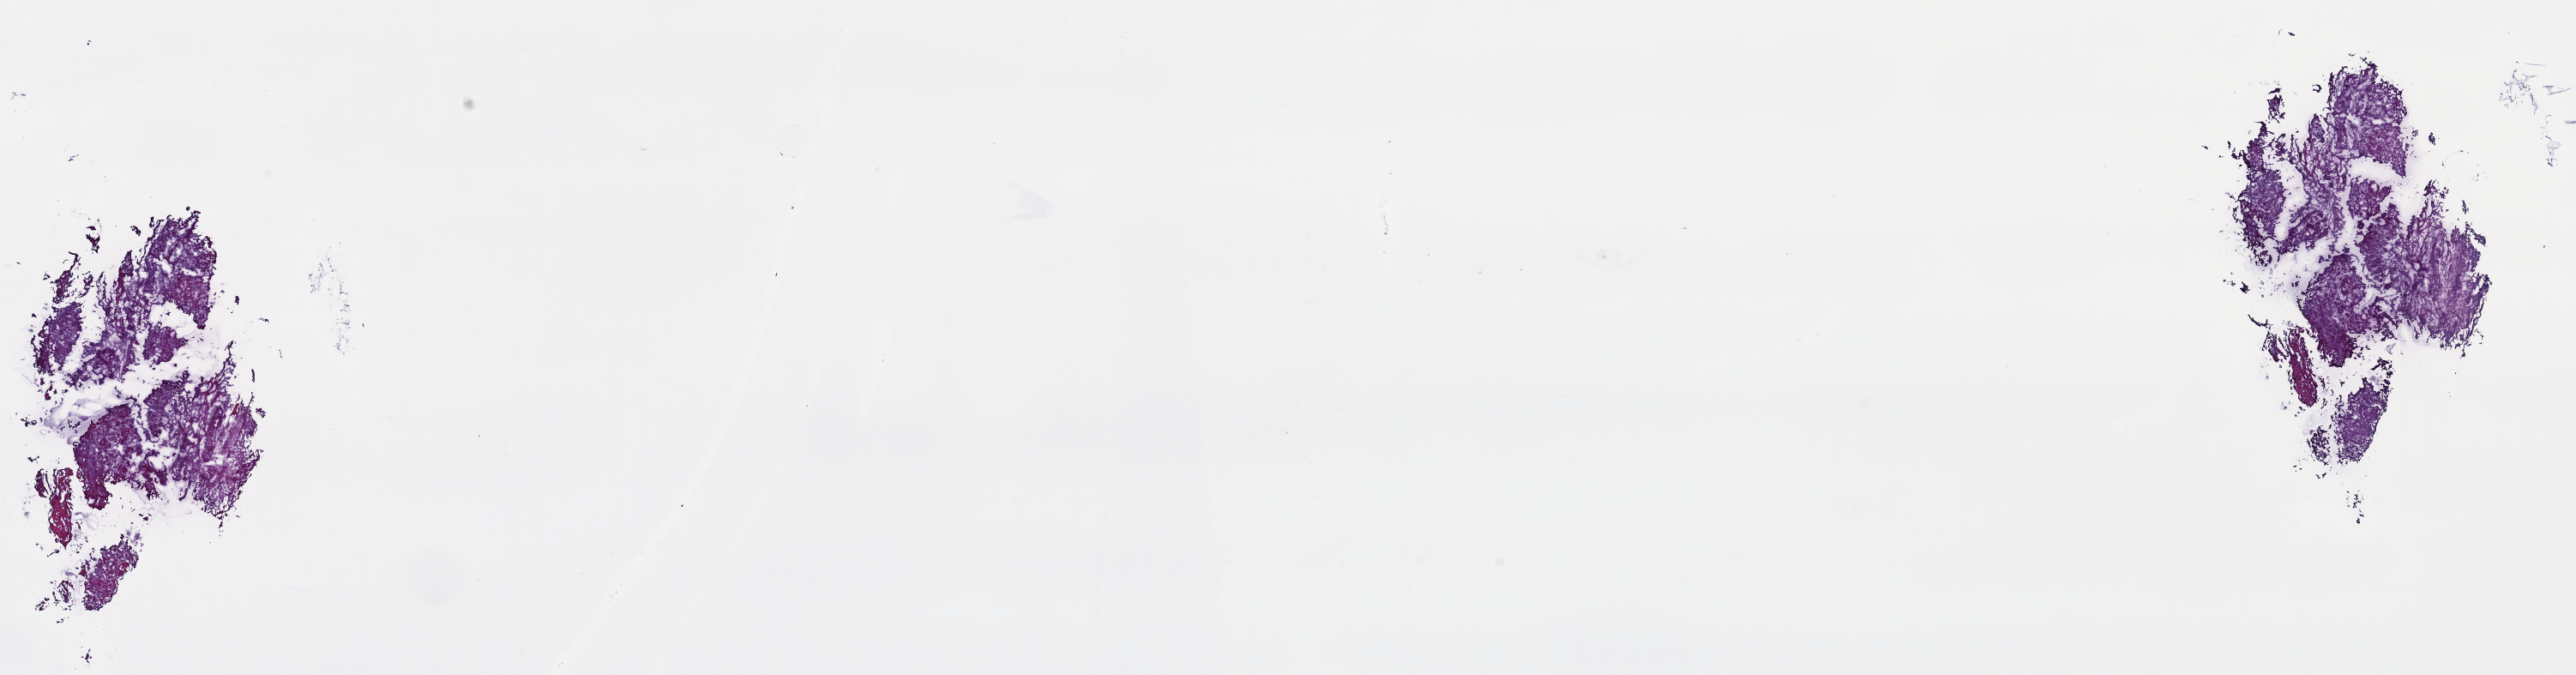
Digitized Hematoxylin and eosin (H&E) stained tissue section (whole slide) — shown as a low-resolution overview of the whole scanned area (about 23.6 x 6.2 mm, acquisition: 40x scan); frozen section from the top of the tissue portion; head and neck, primary tumour sample. Male, age 65 years at initial diagnosis. Histologic grade: G2 (moderately differentiated). Slide review estimates, as recorded: tumour cells 70%, tumour nuclei 90%, normal cells 0%, stromal cells 20%, necrosis 10%. Inflammatory infiltration, as recorded: lymphocyte infiltration 0%, monocyte infiltration 0%, neutrophil infiltration 0%.
AJCC pathologic stage: II (7th edition). Diagnosis: Squamous cell carcinoma, NOS (tongue, NOS).